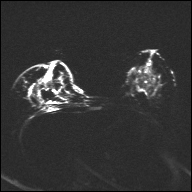
Breast MRI, one axial slice. Slice 17 of 32 in the series (ordered by position). Diffusion-weighted series; image 2 of 4 stored at this slice position (different b-values; order by instance number). 1.5 T. 4 mm slice thickness. 192 × 192 image matrix. Female patient.
Annotated regions visible in this slice (expert manual segmentation):
- tumour on diffusion-weighted imaging: bounding box <49,81,57,85> (left, top, right, bottom; pixels)